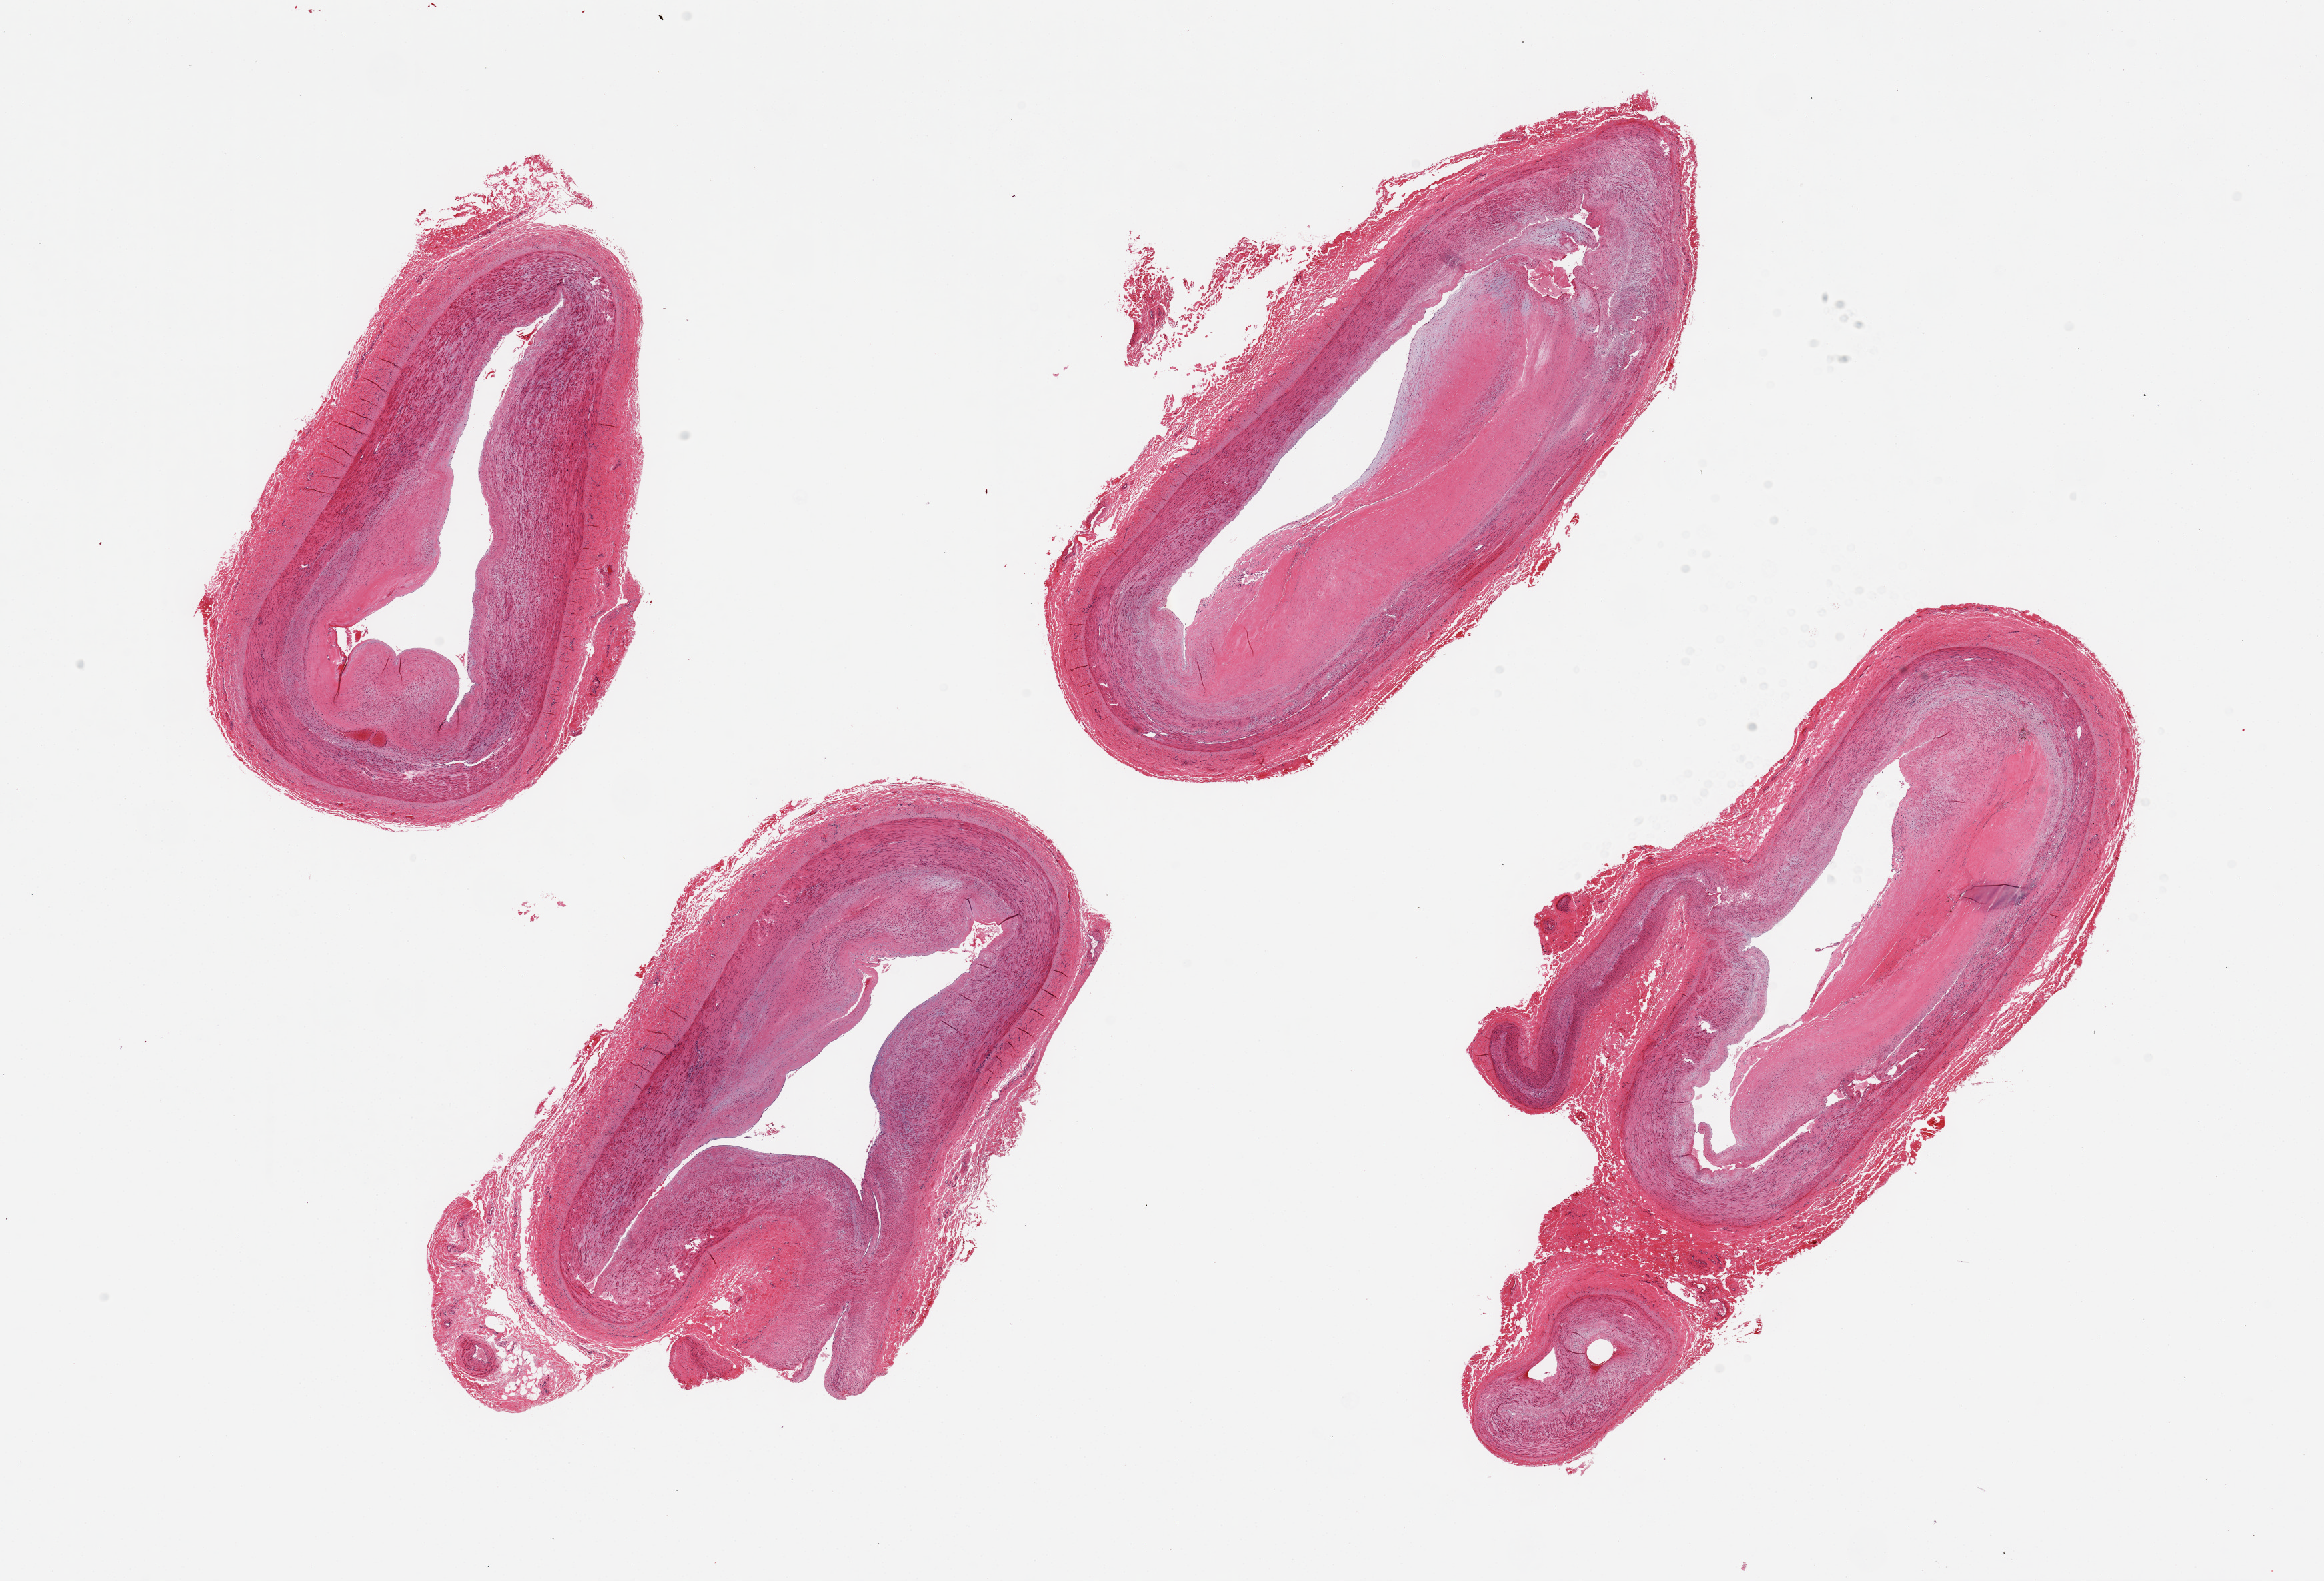
Whole-slide image, hematoxylin and eosin (H&E) stain — whole scanned area (about 27.6 x 18.8 mm) shown as a low-resolution overview, PAXgene-fixed paraffin-embedded (PFPE) section, sampled site (target tissue): tibial artery, tissue donor sample. Donor sex: male.
Review note (as recorded): 4 pieces. Large fibrotic plaques narrow up to 60% of lumen.